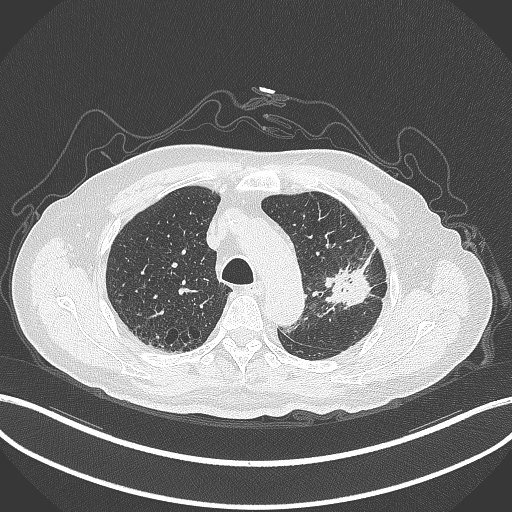
Chest CT, one axial slice. 120 kVp. Lung window (W 1500 / L -600 HU). 1 mm slice thickness. 512 × 512 image matrix, field of view 400 × 400 mm. Male patient, age 79 years. Case-level facts recorded for this patient, not image findings: clinical TNM (as recorded): T2a N1 M1.
Outlined on this slice (rectangle marked by the reading radiologist):
- lung tumour (recorded histology: adenocarcinoma): box from (x=322, y=246) to (x=385, y=309) px